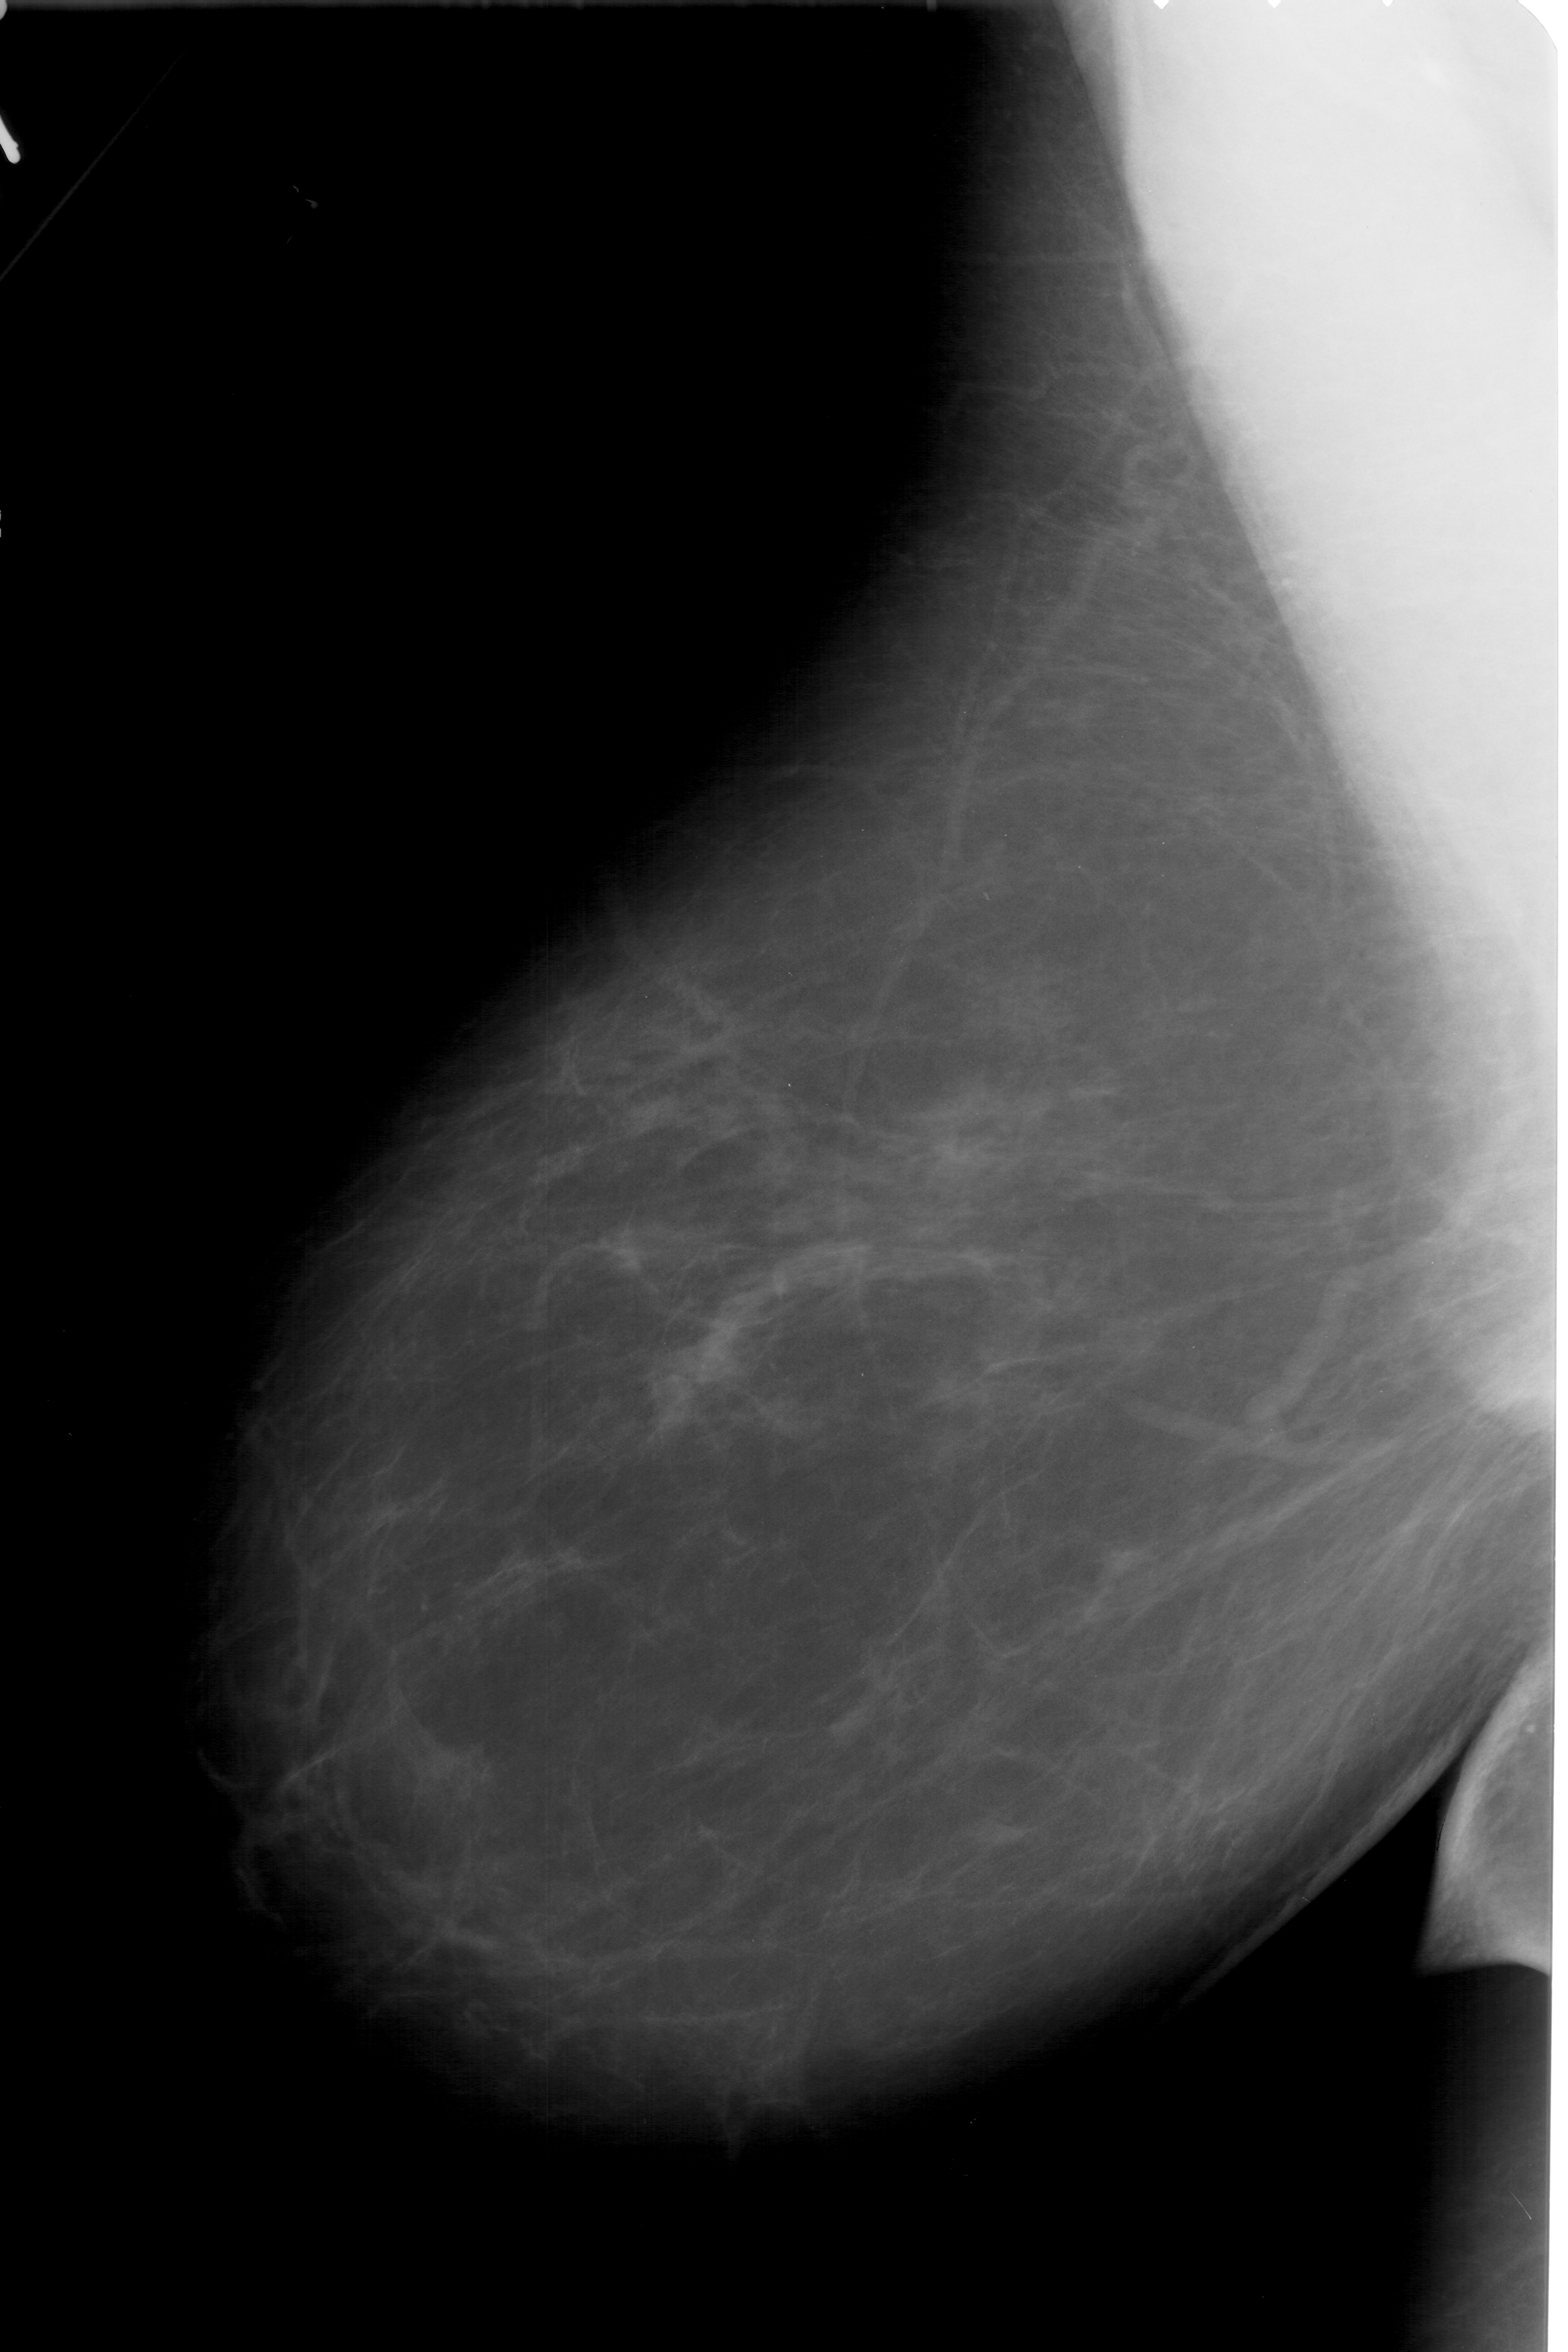
Scanned film-screen mammogram; left breast; MLO view; BI-RADS breast density category 2 (scale 1–4).
Marked abnormality: calcifications, morphology pleomorphic, distribution clustered; BI-RADS assessment category 4; pathology result (as recorded, not read from the image): malignant.